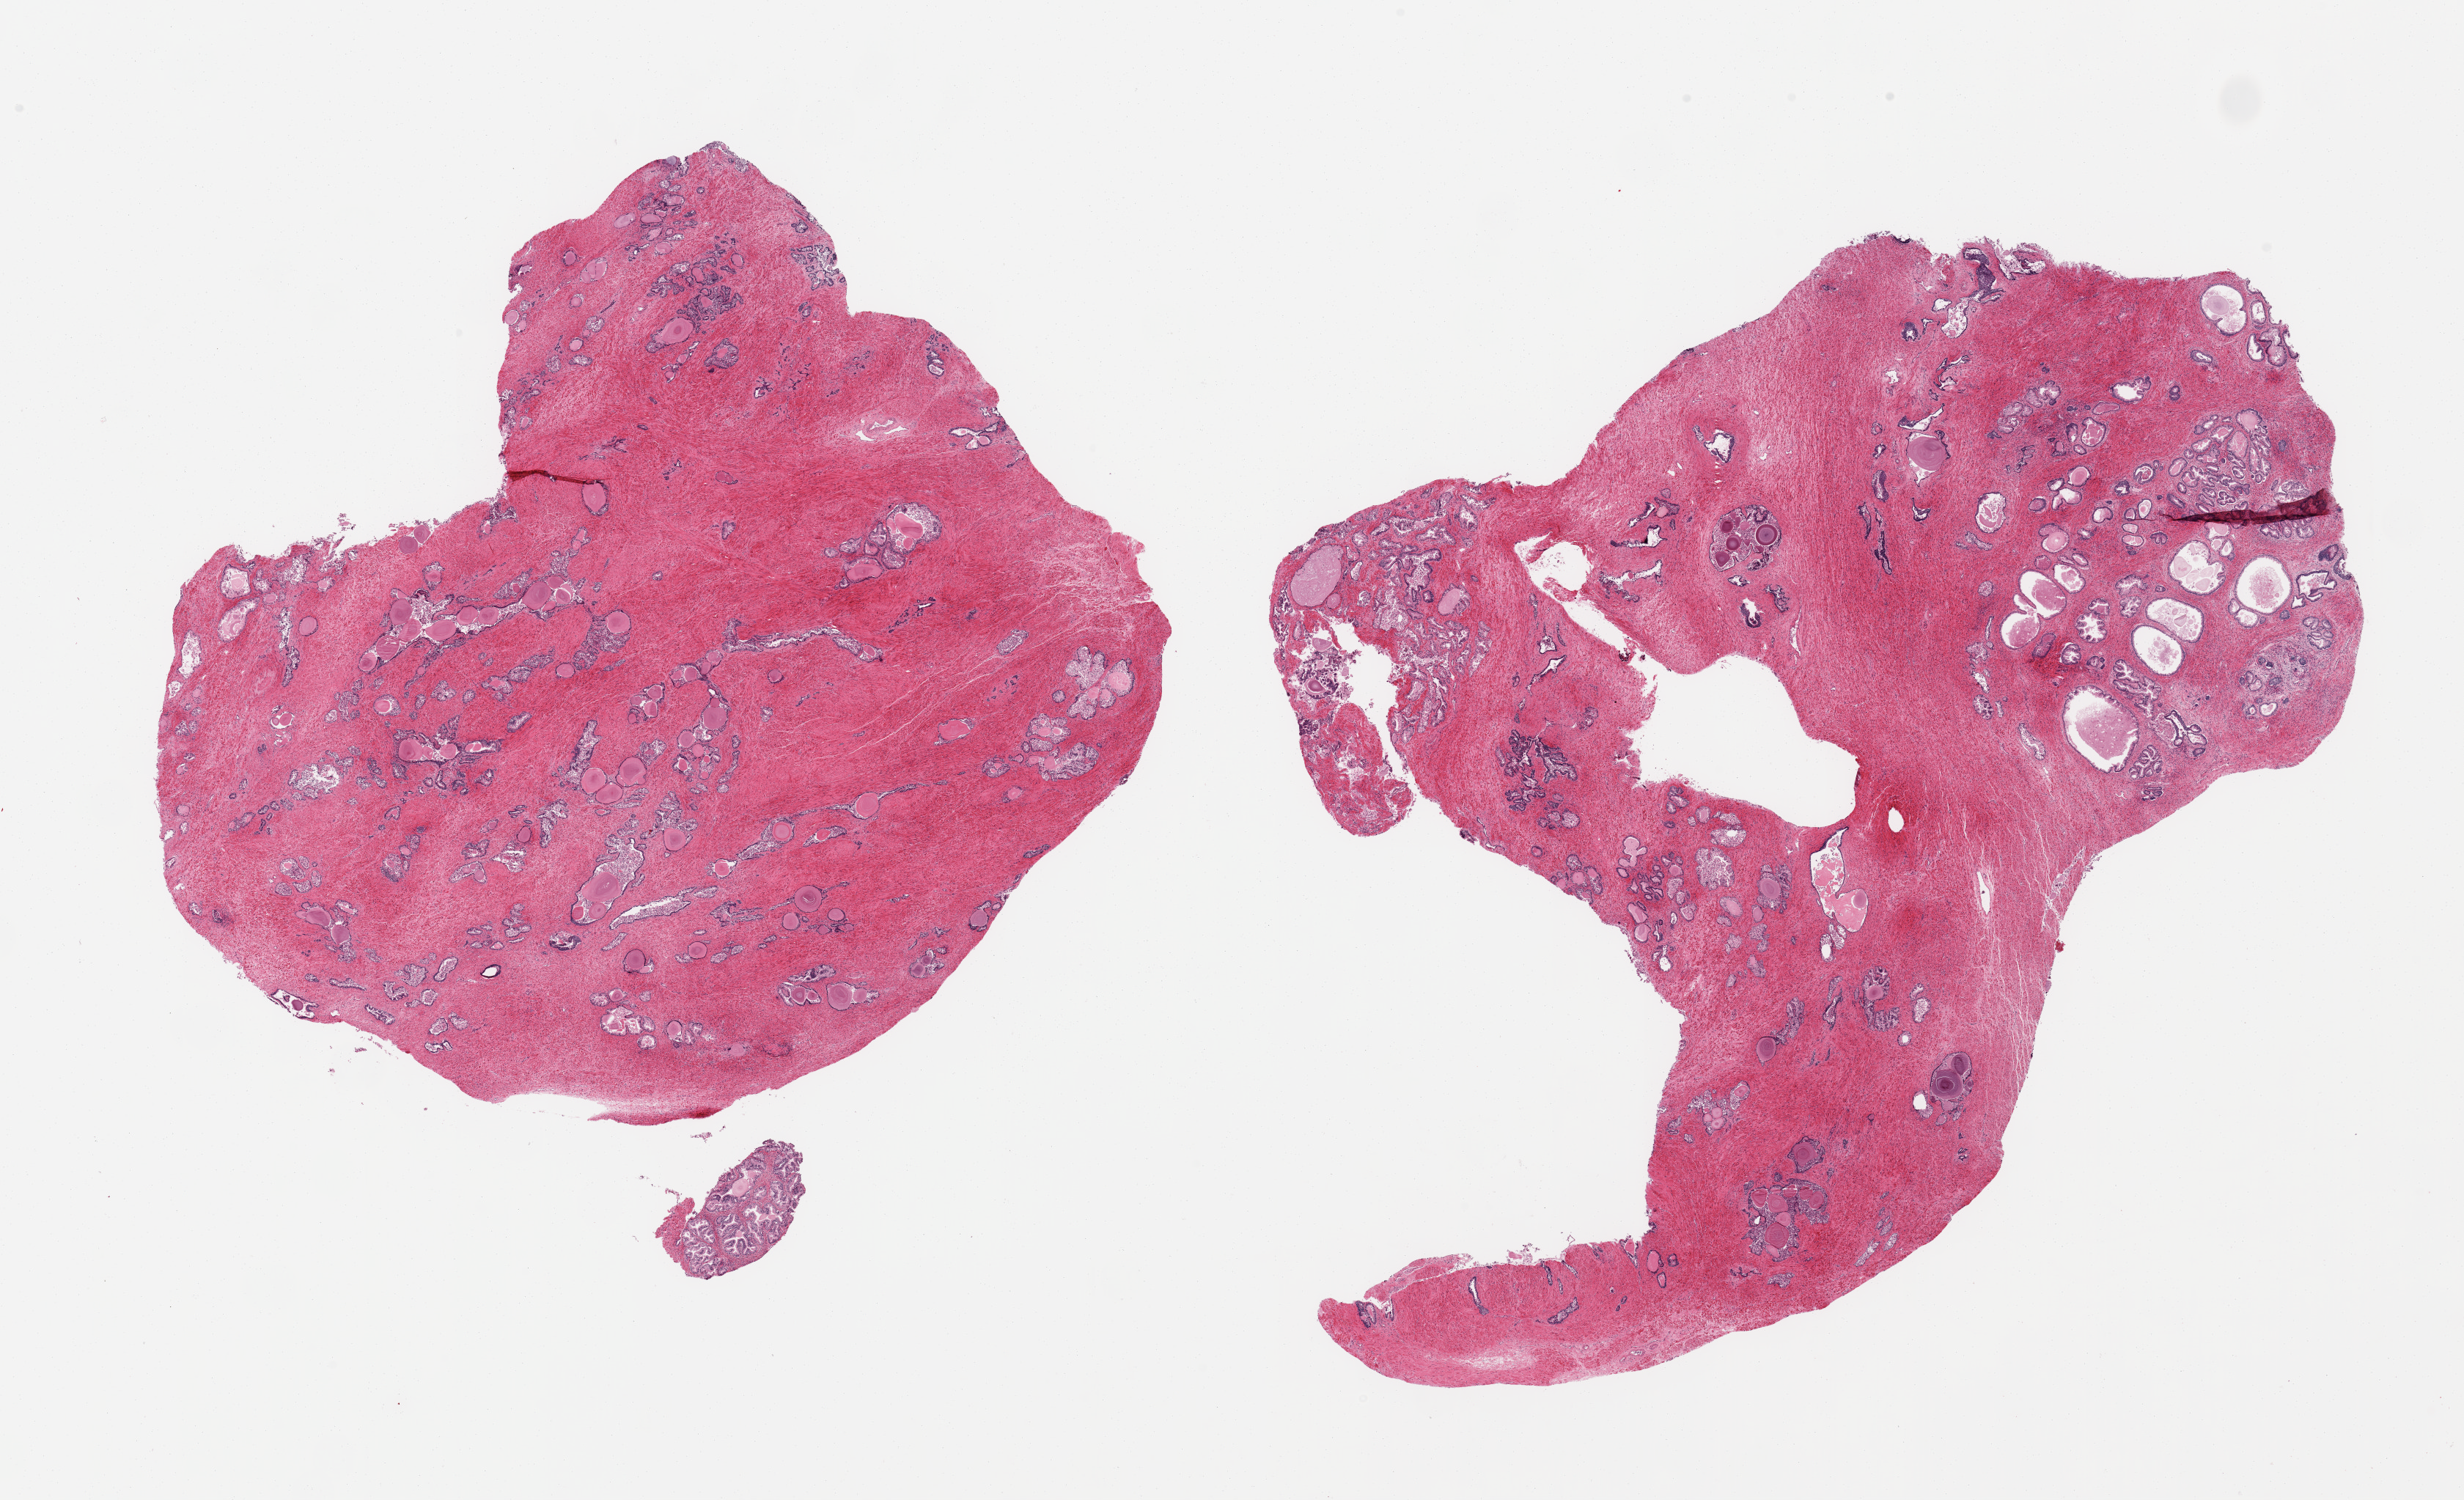
Digitized haematoxylin and eosin-stained section, brightfield — shown as a low-resolution overview of the whole scanned area (about 26.6 x 16.2 mm); PAXgene-fixed paraffin-embedded (PFPE) section; section of prostate (target tissue); tissue donor sample.
Reviewer comment on this tissue sample: 2 pieces; glands poorly preserved, stroma intact.